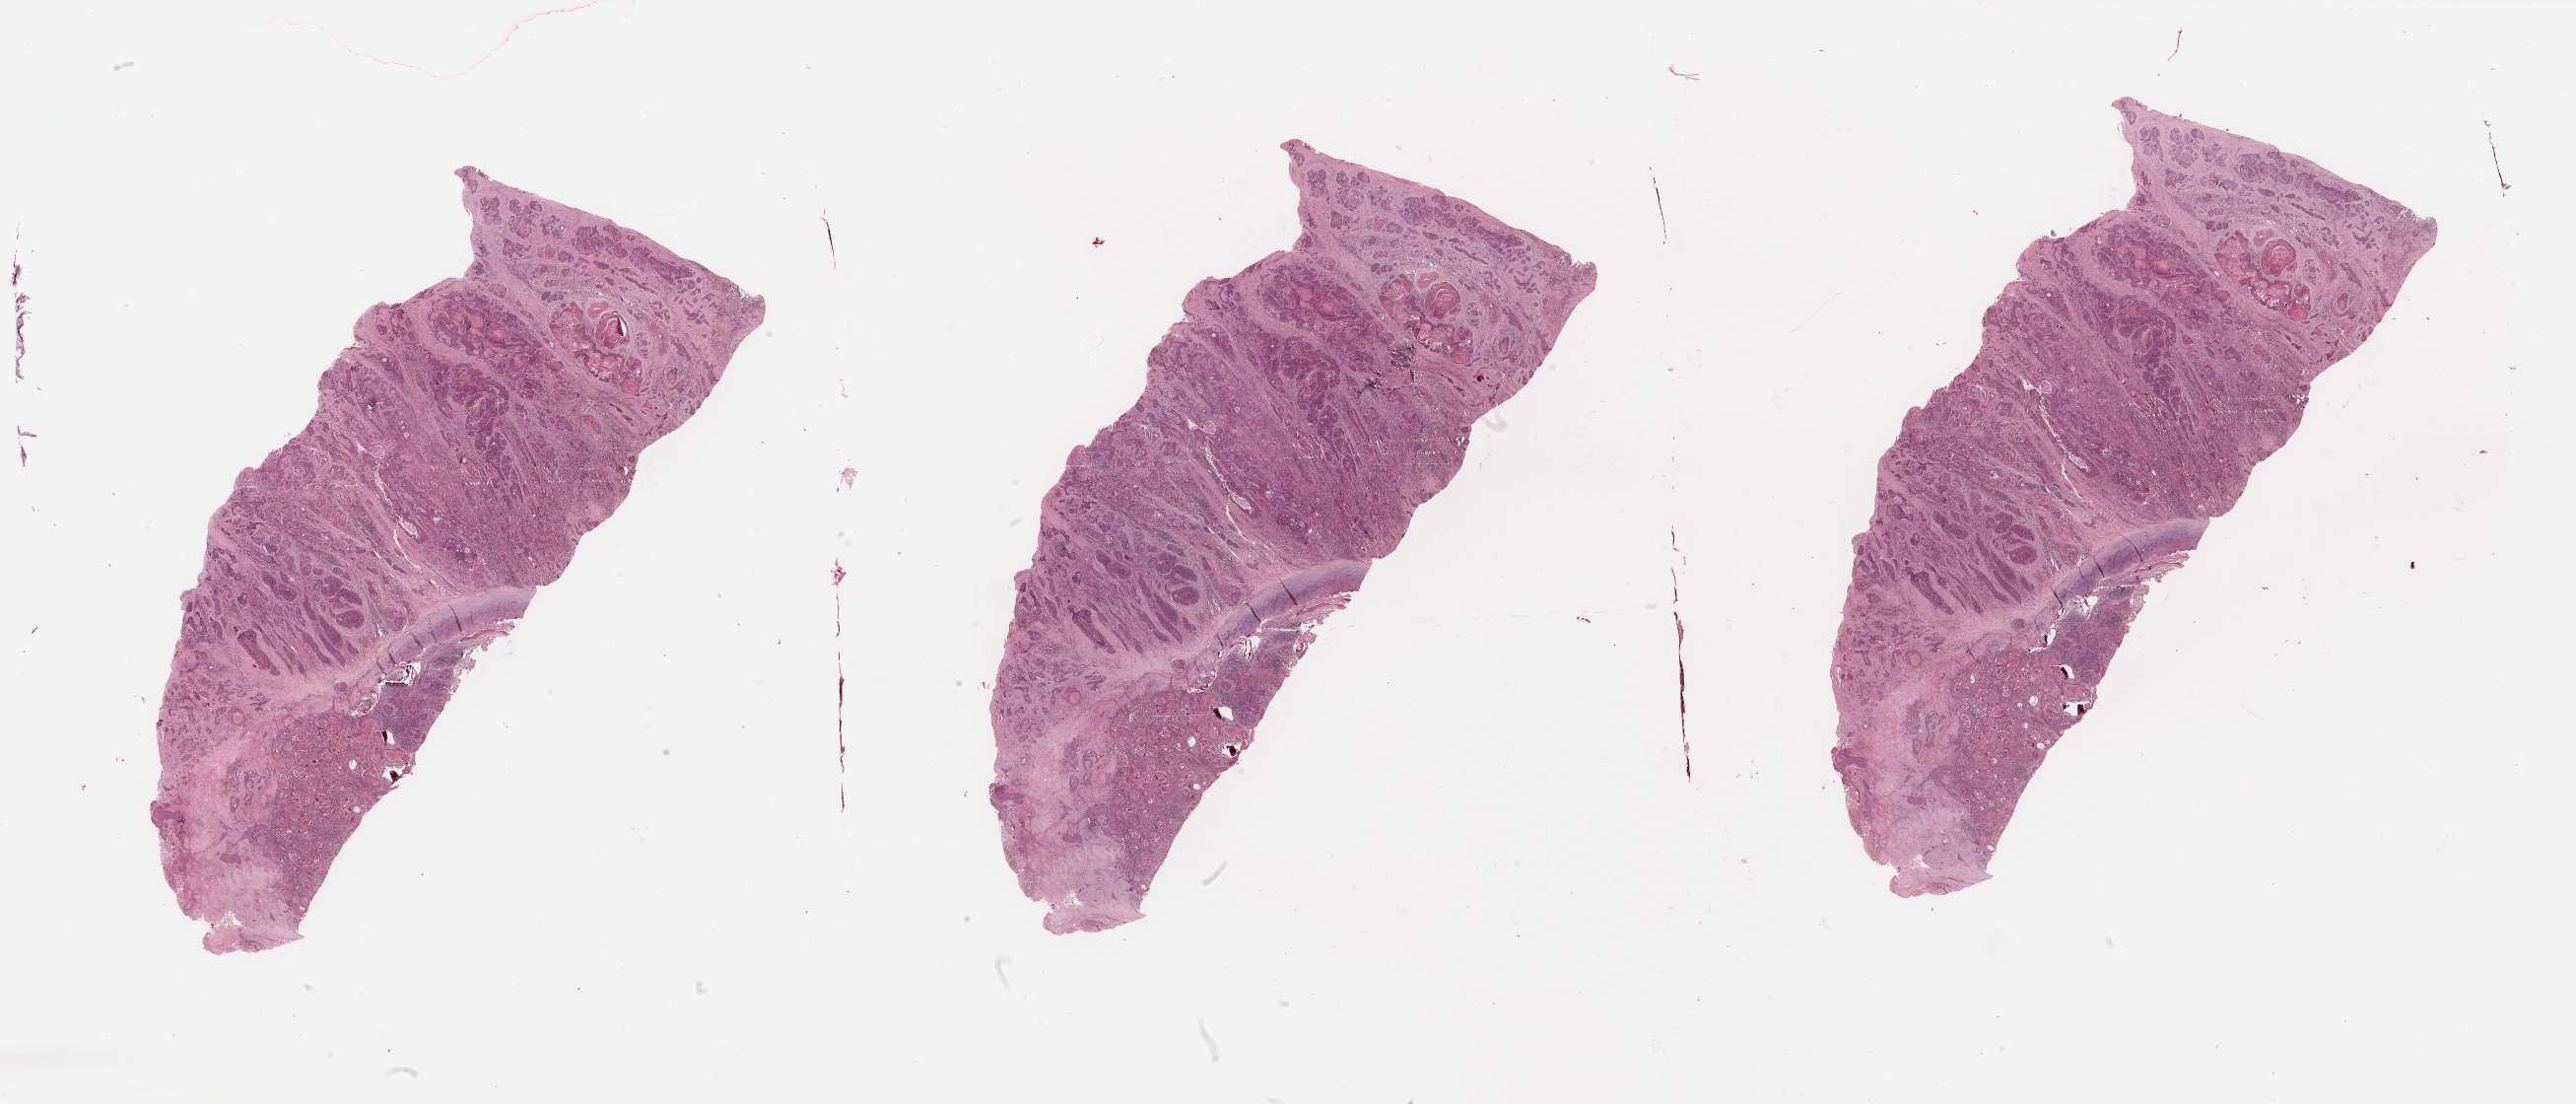
Hematoxylin and eosin (H&E) stained whole-slide image, low-resolution overview of the scanned area, about 41.3 x 17.7 mm (slide scanned at 20x). Head and neck, tissue type not recorded. Male, 81 y/o.
- patient diagnosis: Squamous cell carcinoma, NOS (larynx, NOS)